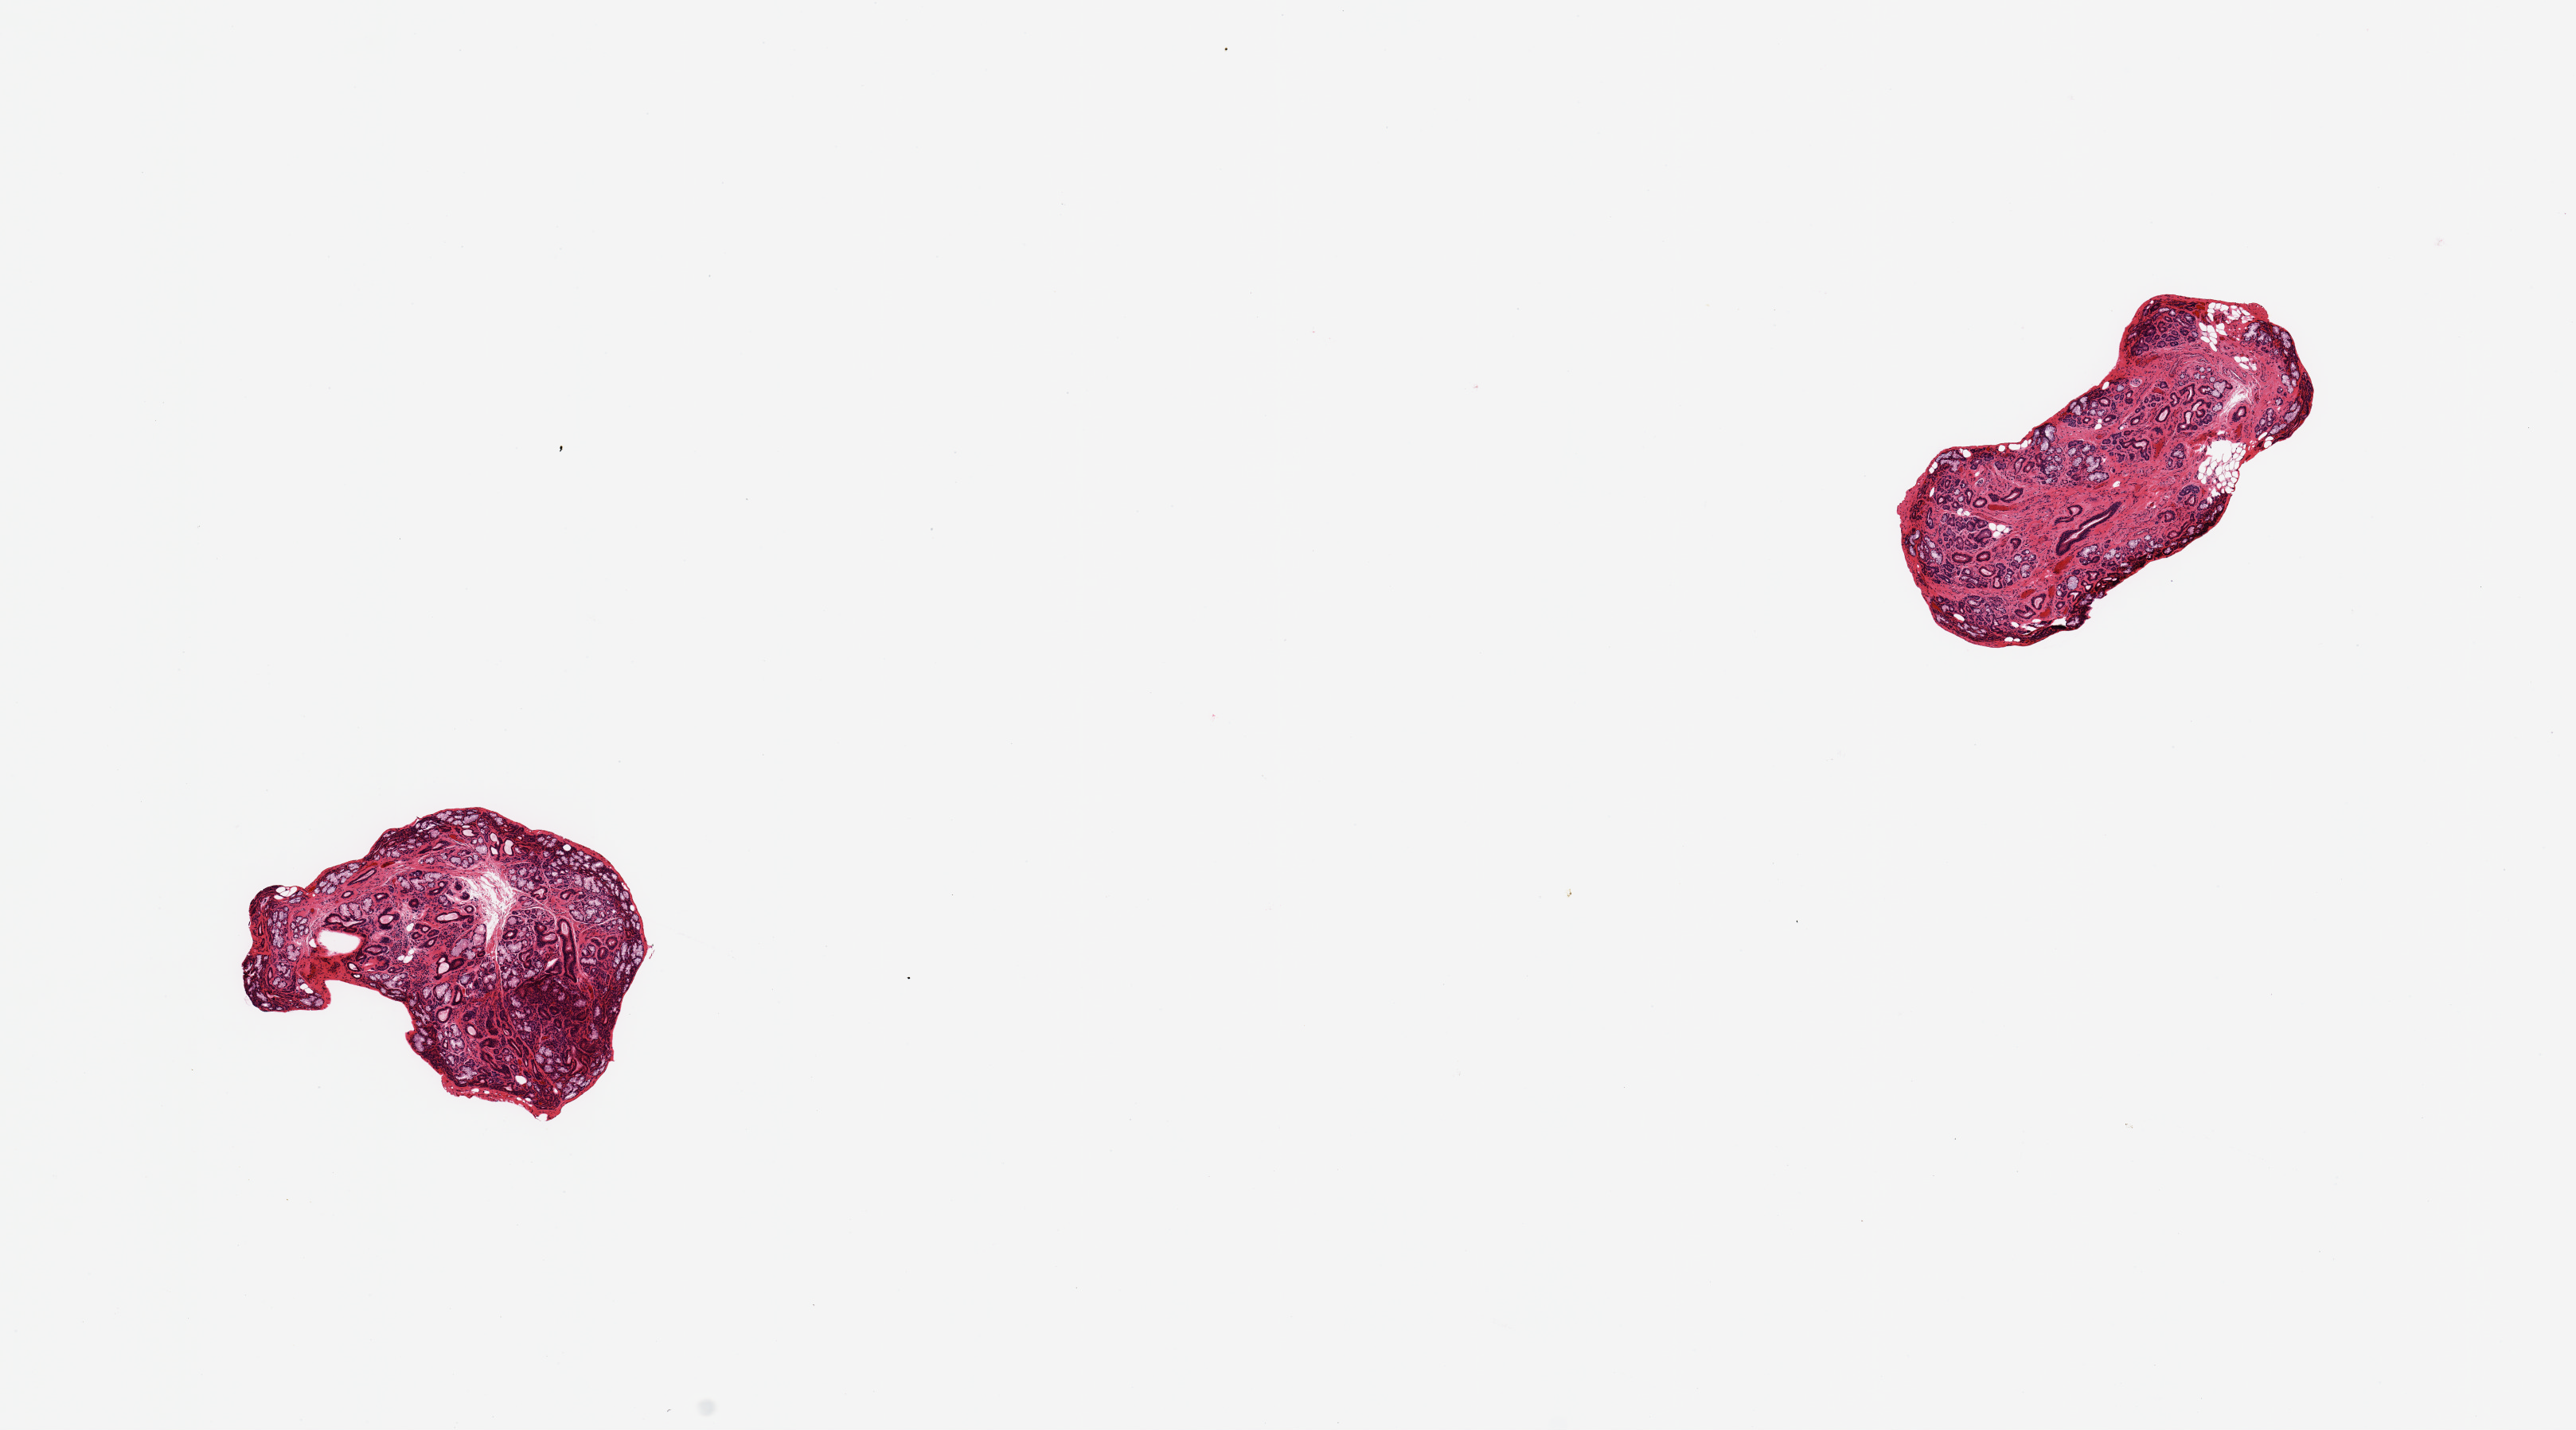
Whole-slide image, hematoxylin and eosin (H&E) stain, brightfield — shown as a low-resolution overview of the whole scanned area (about 12.8 x 7.1 mm). PAXgene-fixed paraffin-embedded (PFPE) section. Section of minor salivary gland (target tissue). Tissue donor sample. Donor: male.
Review note (as recorded): 2 pieces; ~5% to 10% internal fat.